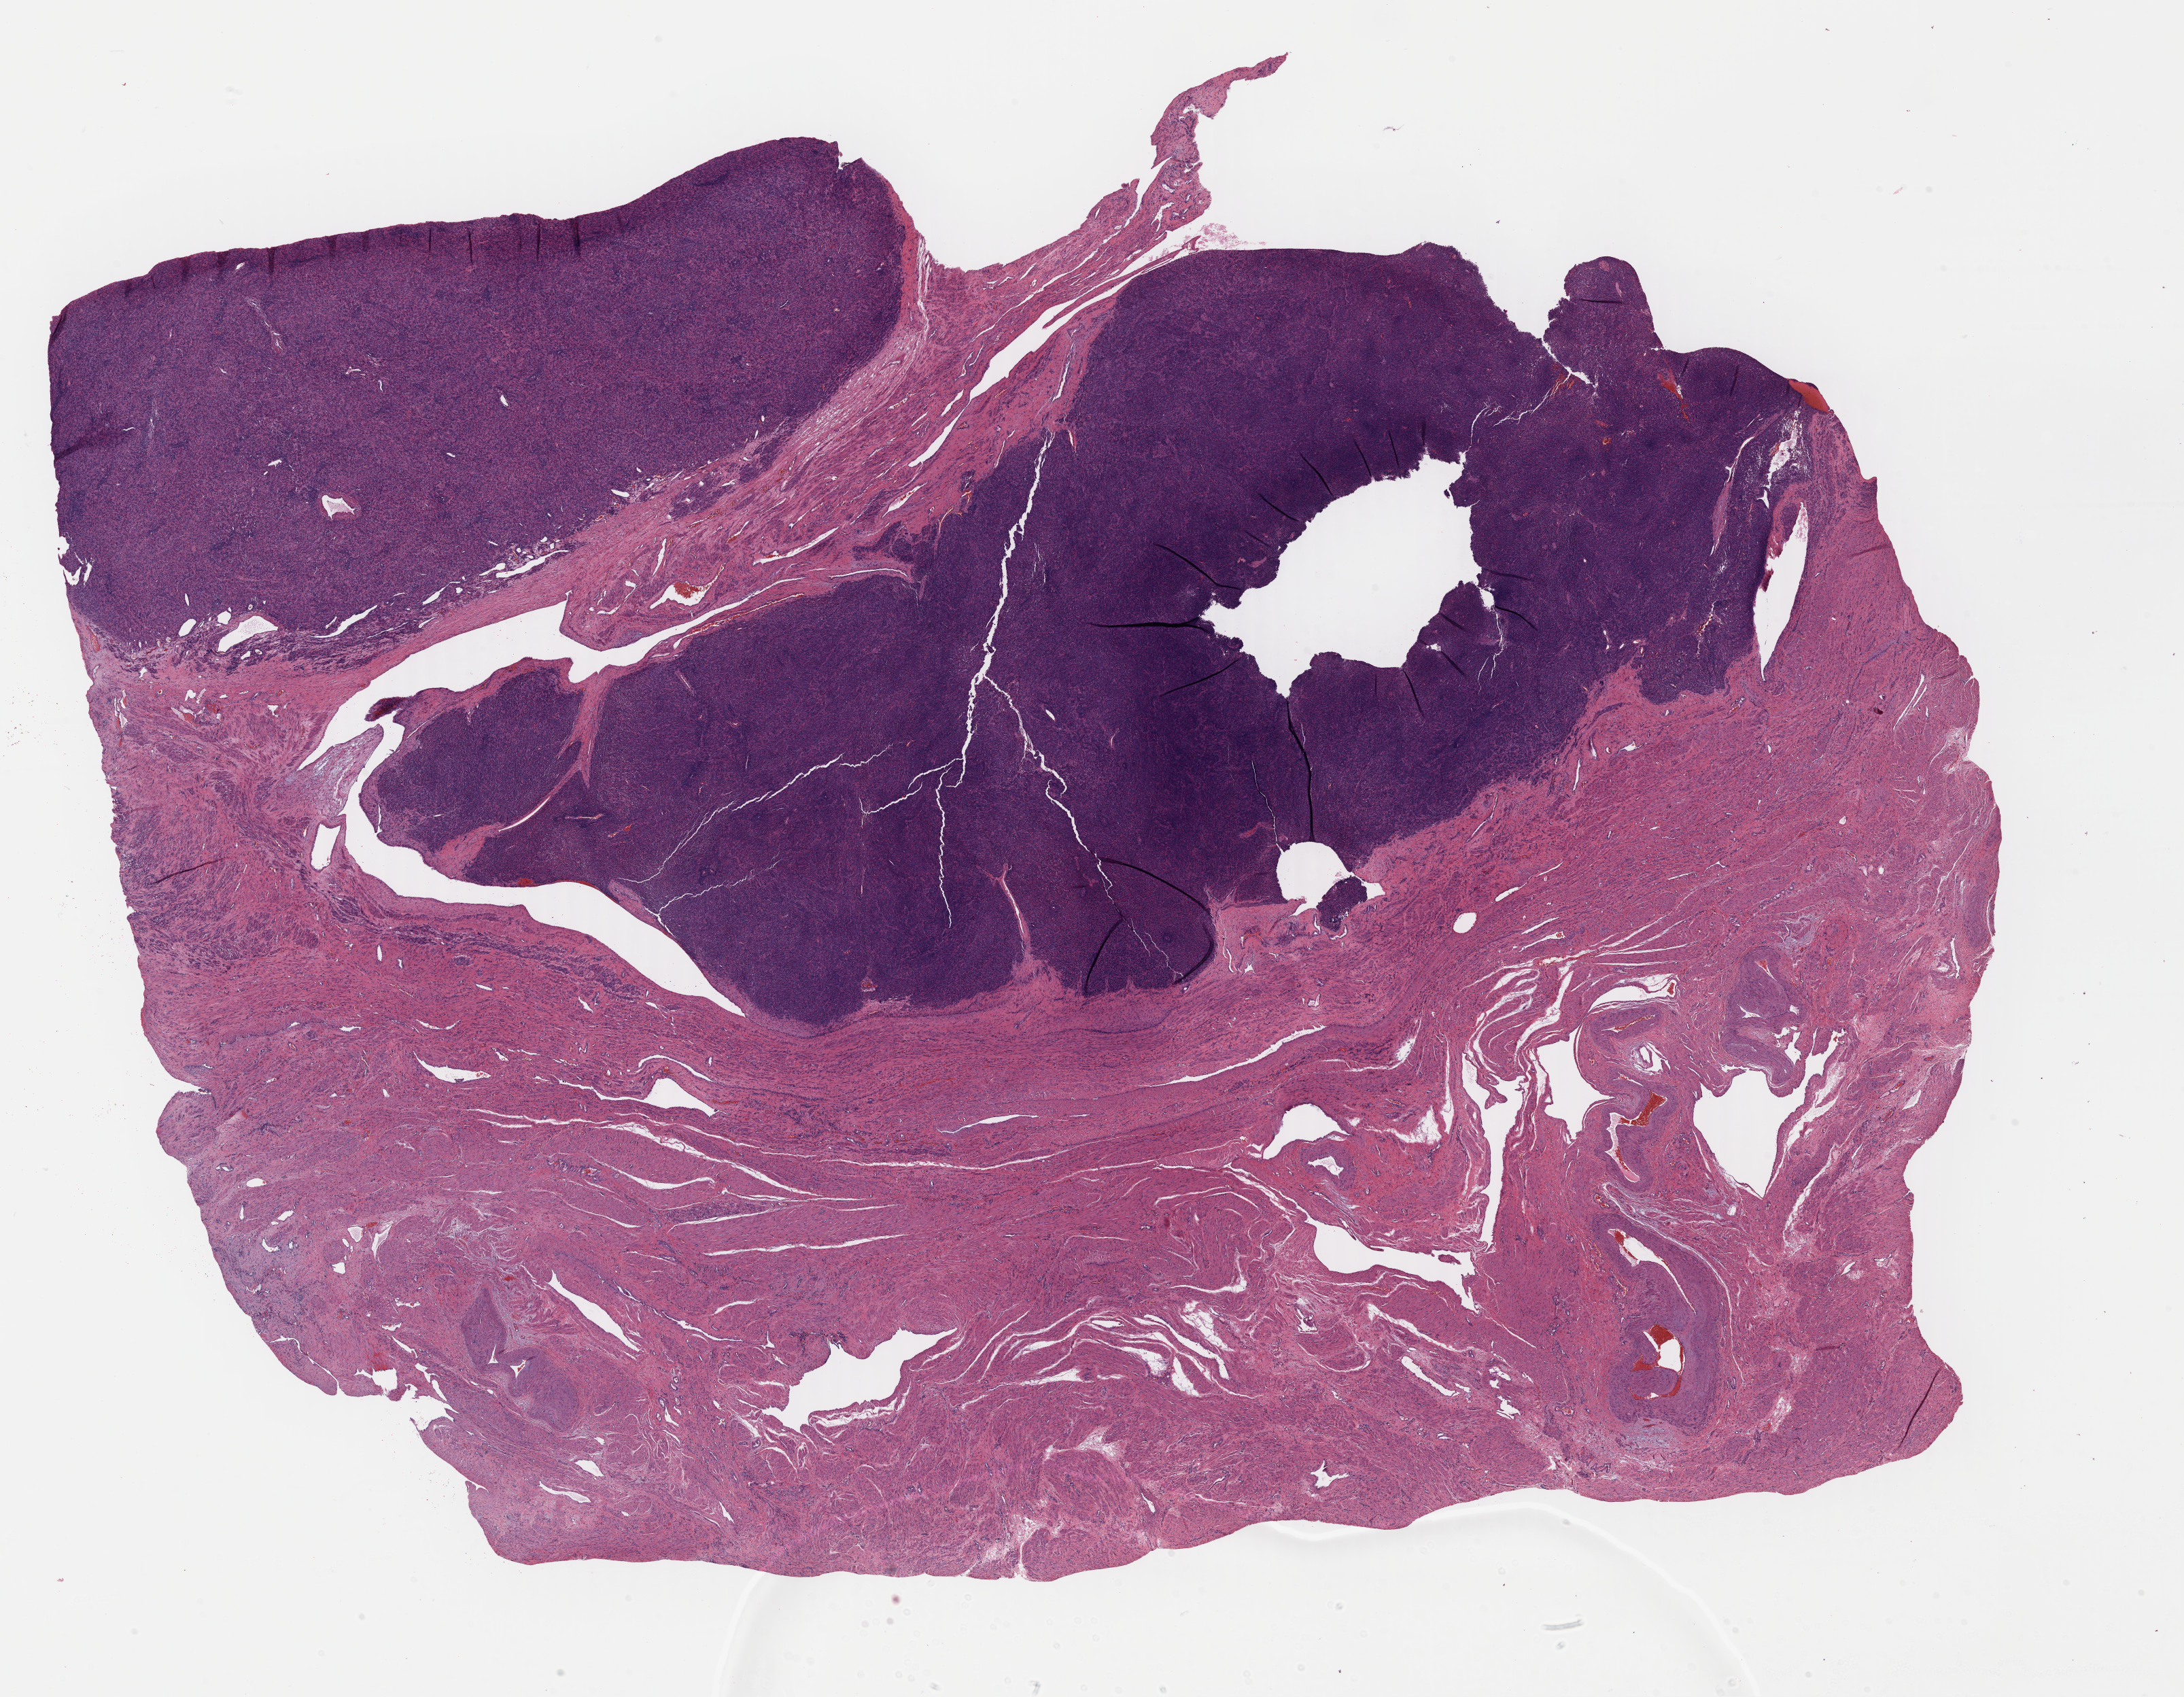
Digitized H&E tissue section (whole slide), shown as a low-resolution overview of the whole scanned area (about 25.3 x 19.6 mm). Formalin-fixed paraffin-embedded (FFPE) diagnostic section. Sample: primary tumour, uterus. Female, age 62 years at initial diagnosis.
Diagnosis: Leiomyosarcoma, NOS.